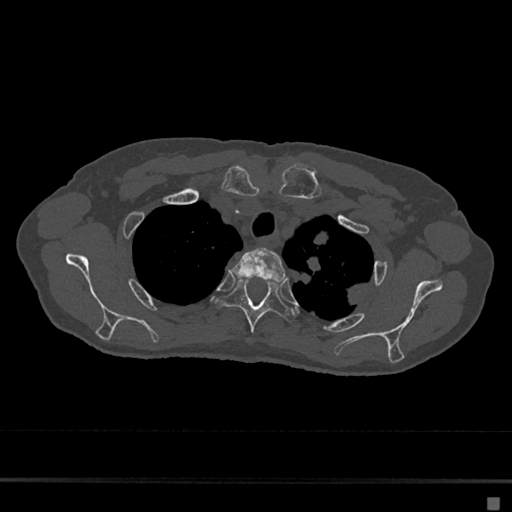
CT including the spine, one axial slice. Slice 550 of 797 in the series (ordered by position). Reconstruction kernel Br40s/3. 120 kVp. Bone window (W 1800 / L 400 HU). 0.5 mm slice thickness. 512 × 512 image matrix. Female patient, age 68 years. Case-level facts recorded for this patient, not image findings: primary cancer: renal.
Structures marked on this image (semi-automatic segmentation, software-assisted and operator-edited):
- T2 vertebra: box from (x=232, y=248) to (x=287, y=282) px
- T3 vertebra: (x=218, y=278)–(x=296, y=332)